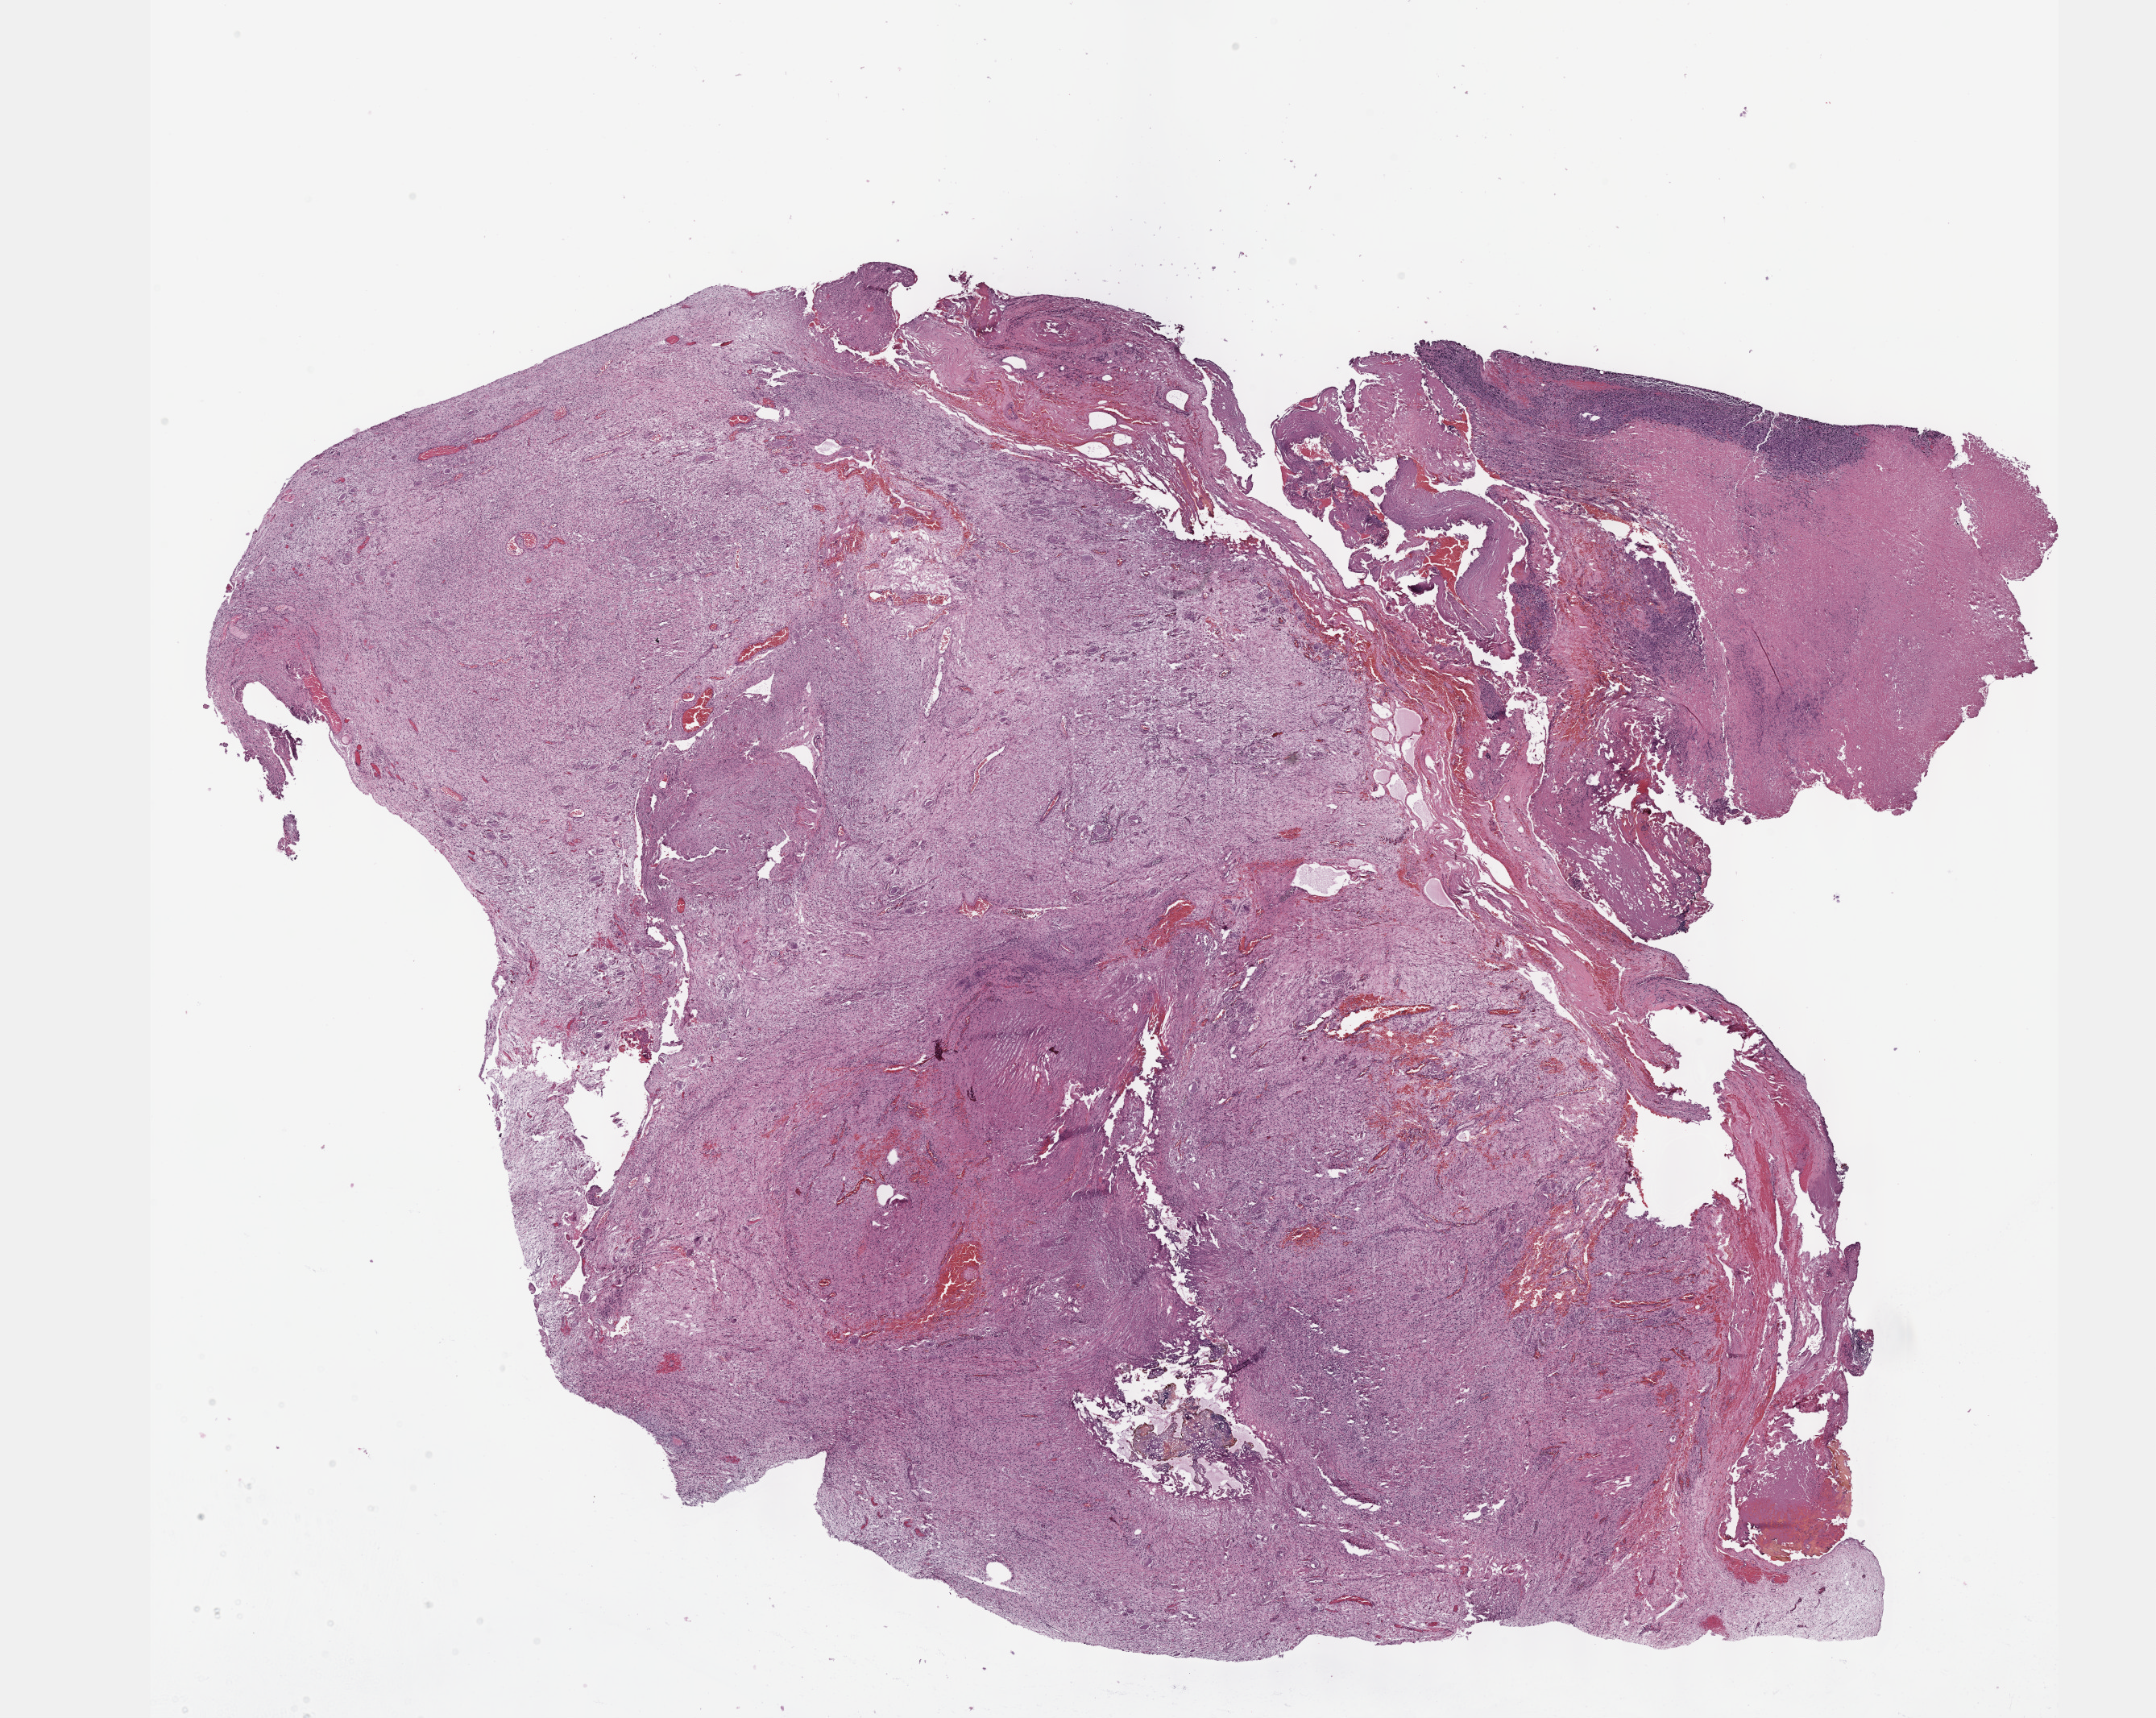
Whole-slide histology image, H&E-stained, whole scanned area (about 21.6 x 17.2 mm, slide scanned at 40x) shown as a low-resolution overview. FFPE section. Primary tumour sample from the peripheral nerves and autonomic nervous system. Male, age 50 years at initial diagnosis.
Histologic diagnosis: Malignant peripheral nerve sheath tumor.